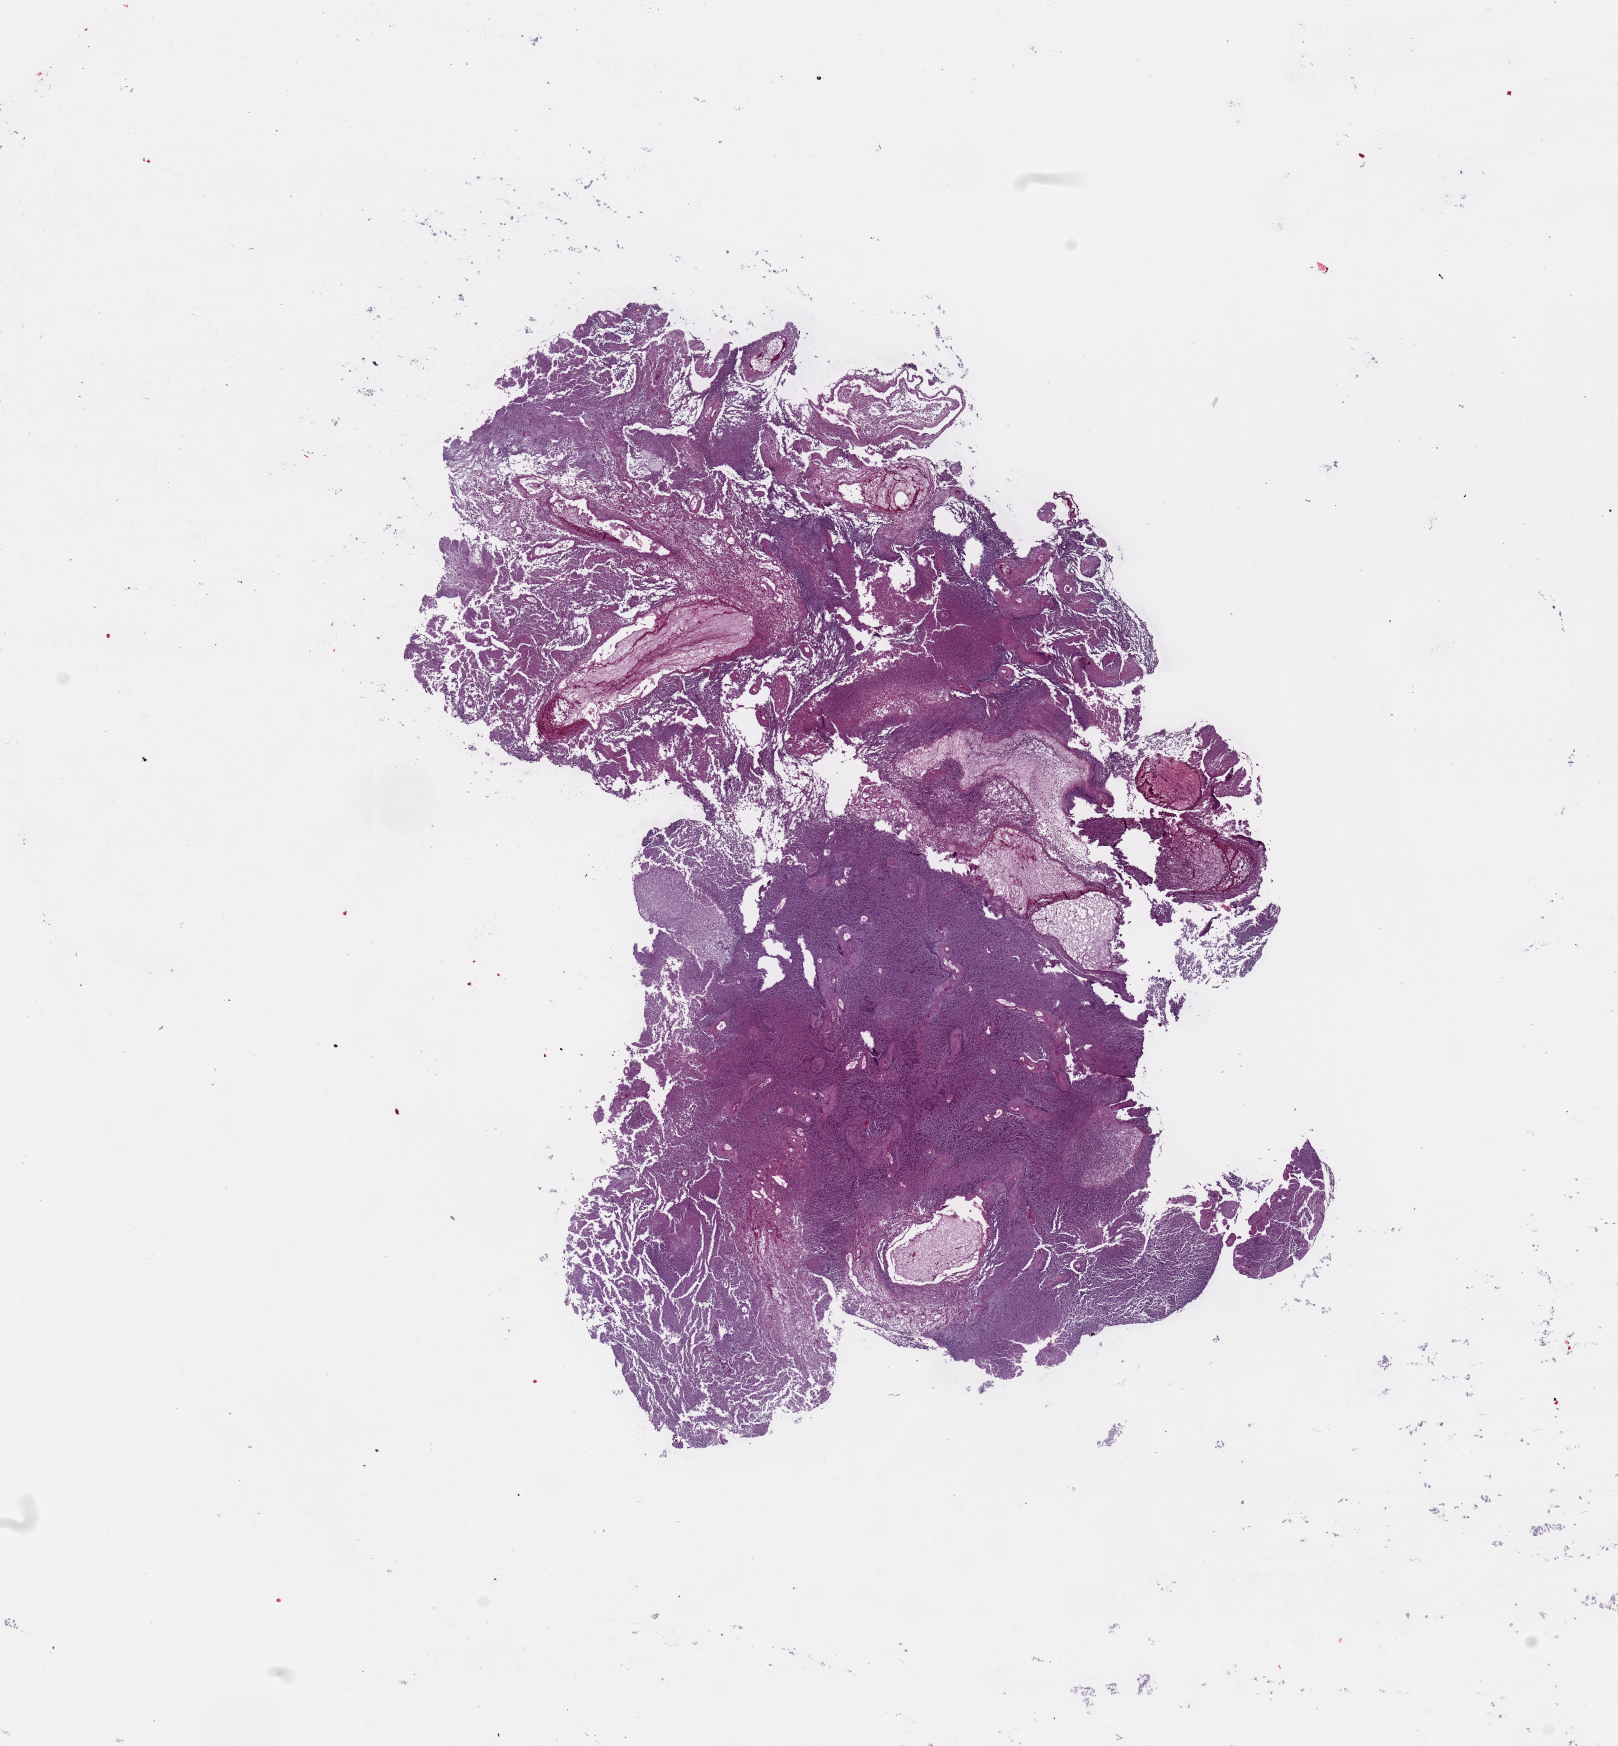
Digitized H&E tissue section (whole slide), a low-resolution overview of the entire scanned area, about 12.8 x 13.8 mm (acquisition: 20x scan). Brain, tumour tissue. Patient: female, age 53 years.
* histologic diagnosis: Glioblastoma
* primary tumour site (as recorded): temporal lobe